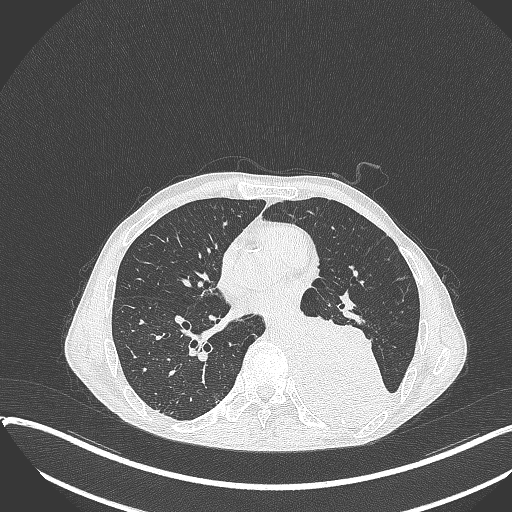
Chest CT, one axial slice. Slice 165 of 401 in the series (ordered by position). Reconstruction kernel B70f. Lung window (W 1500 / L -600 HU). 1 mm slice thickness. 512 × 512 image matrix, field of view 400 × 400 mm. Patient: male, 57 years. Case-level facts recorded for this patient, not image findings: clinical TNM (as recorded): T4 N0 M0.
Annotated regions visible in this slice (bounding box drawn by a radiologist):
- lung tumour (recorded histology: squamous cell carcinoma): bounding box (x1, y1, x2, y2) in pixels: (294, 309, 391, 431)